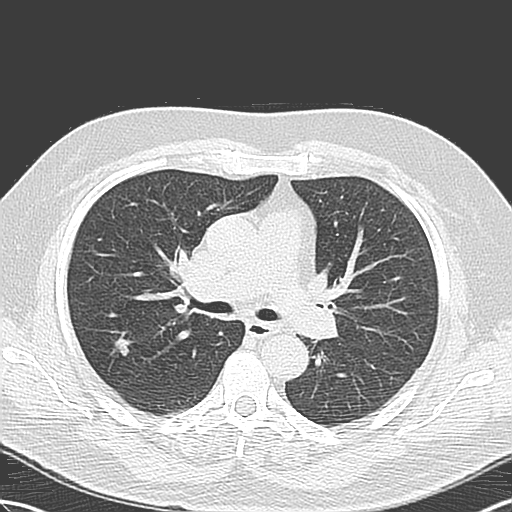
Low-dose screening chest CT, one axial slice. Position 74 of 131 along the scan axis. 120 kVp. Lung window (W 1500 / L -600 HU). 512 × 512 image matrix, field of view 356 × 356 mm.
Outlined on this slice (manually delineated by an expert):
- lesion 1 (tumor, upper lobe of right lung): bounding box [x1, y1, x2, y2] px = [115, 336, 134, 356]